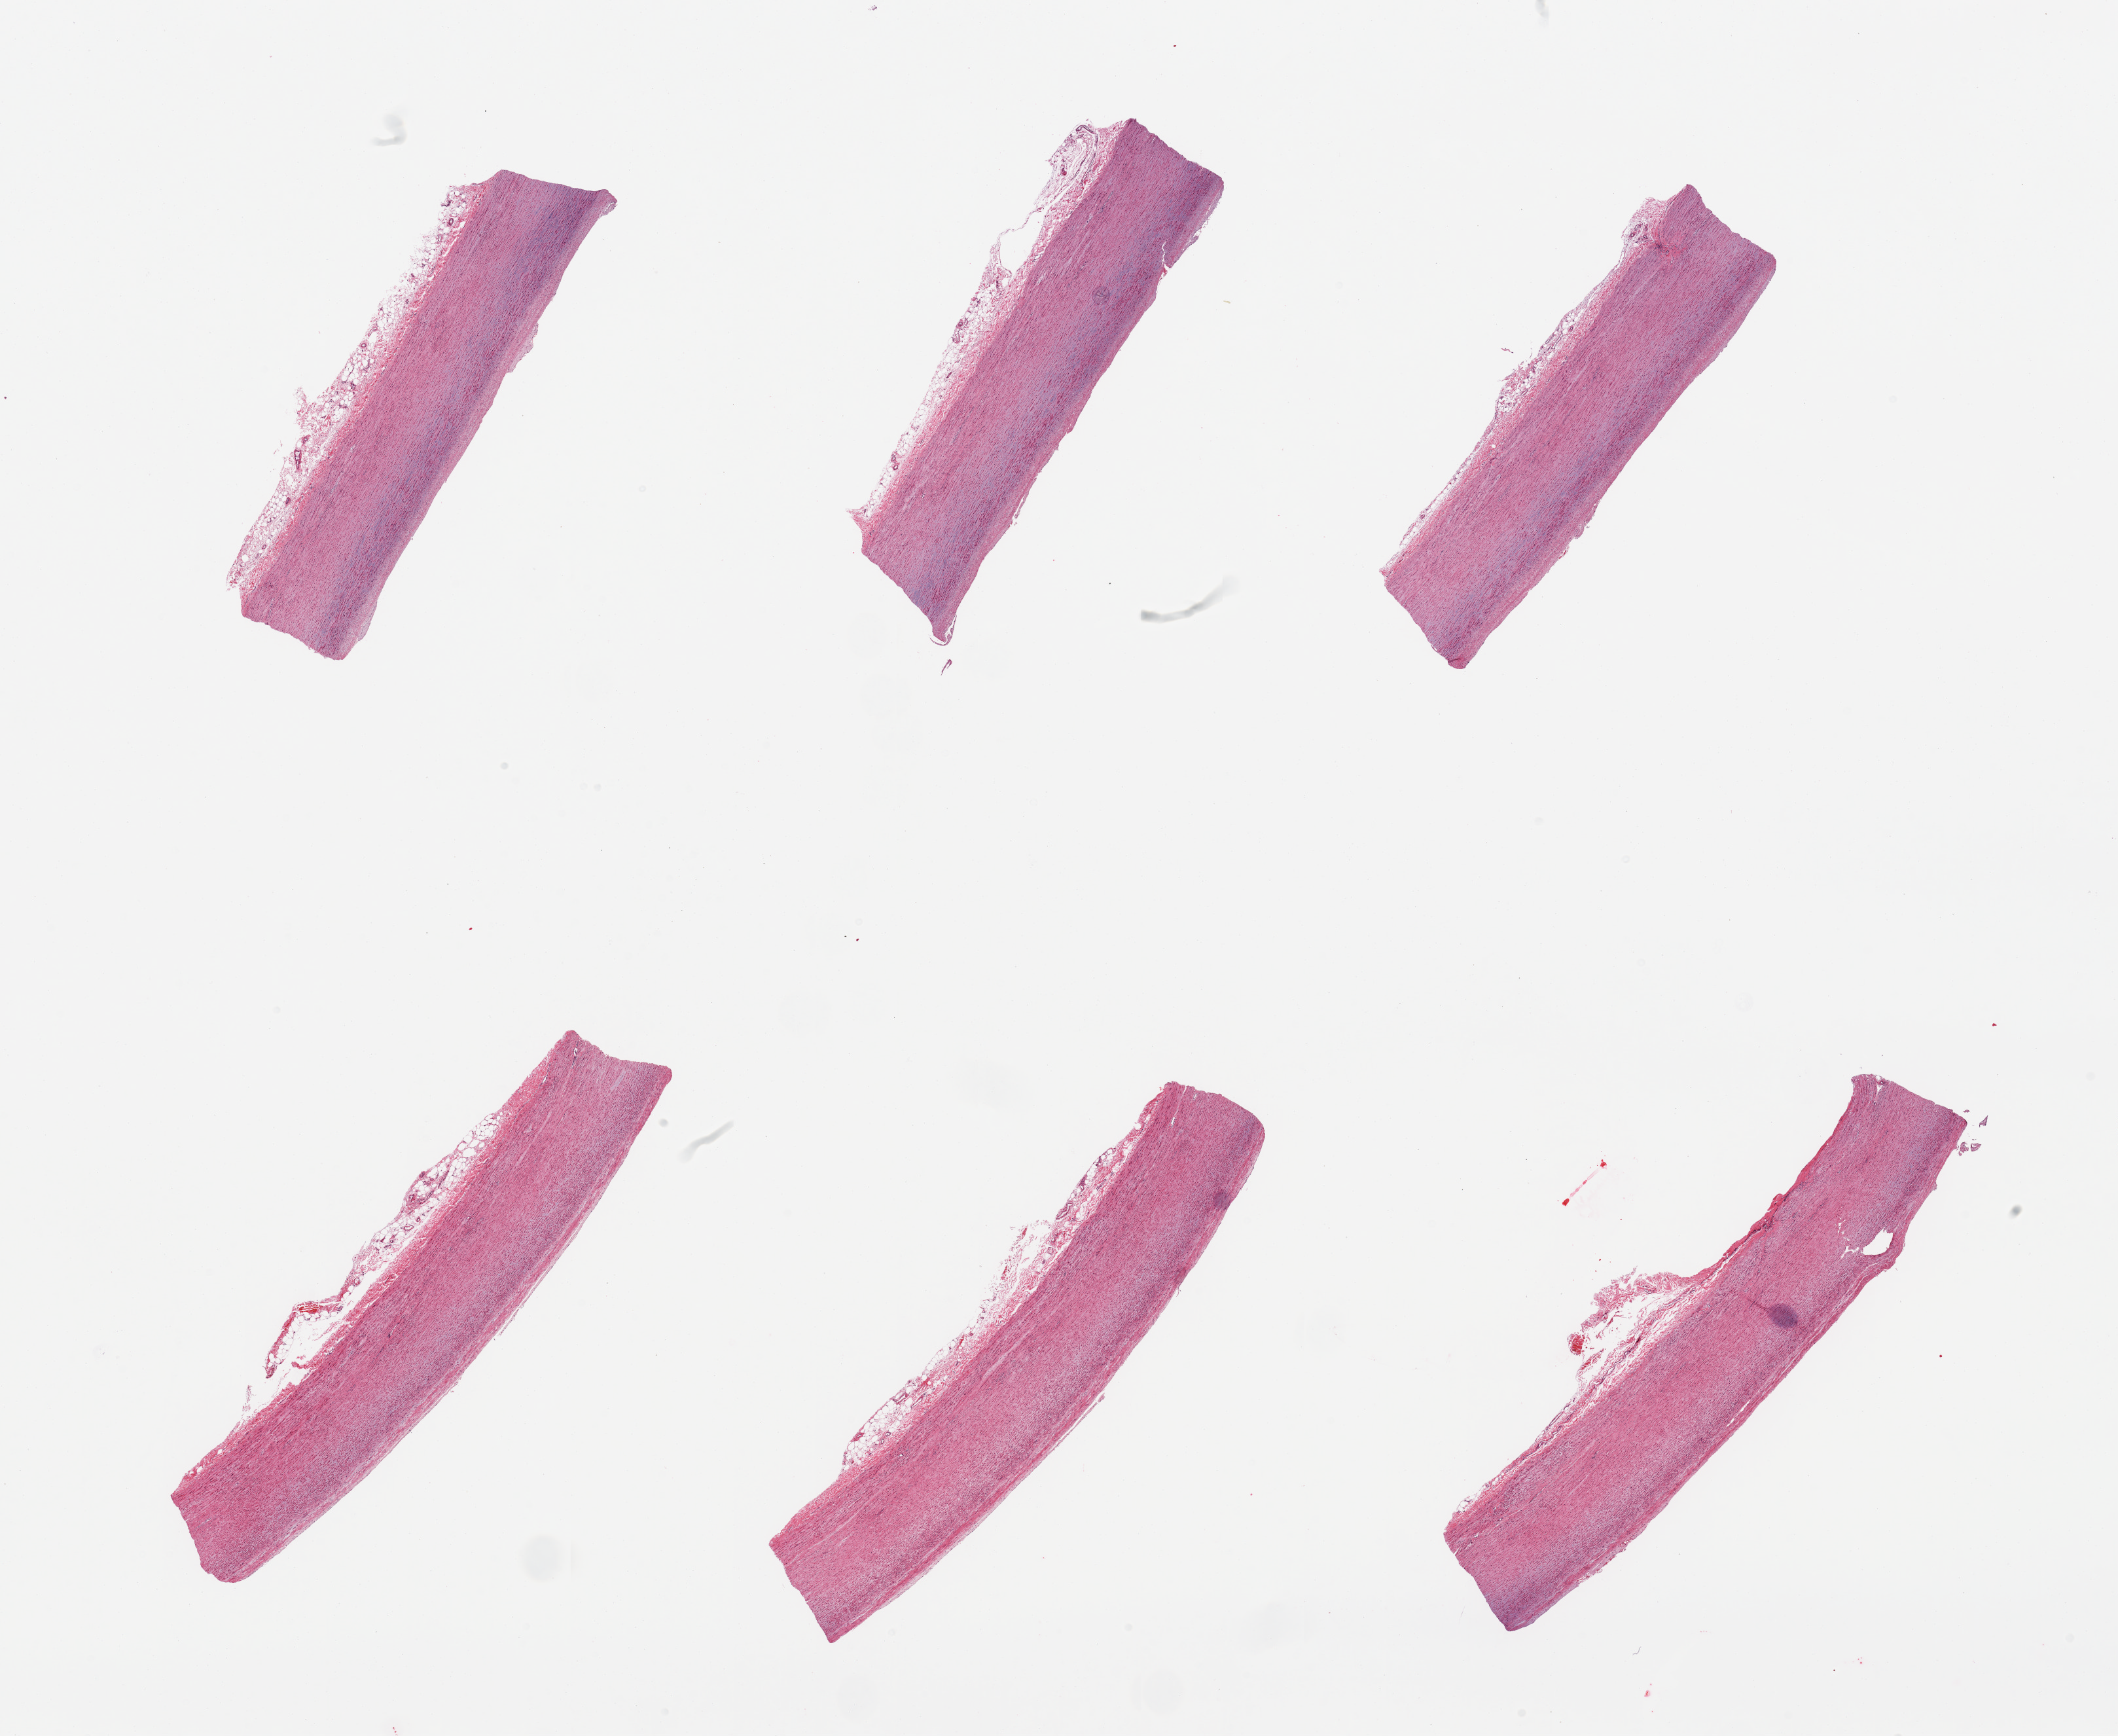
Hematoxylin and eosin (H&E) whole-slide image — low-resolution overview of the scanned area, about 25.6 x 21.0 mm, PAXgene-fixed paraffin-embedded (PFPE) section, target tissue: aorta, donor tissue sample. Donor sex: female.
- review note (as recorded): 6 pieces; well trimmed; no plaques